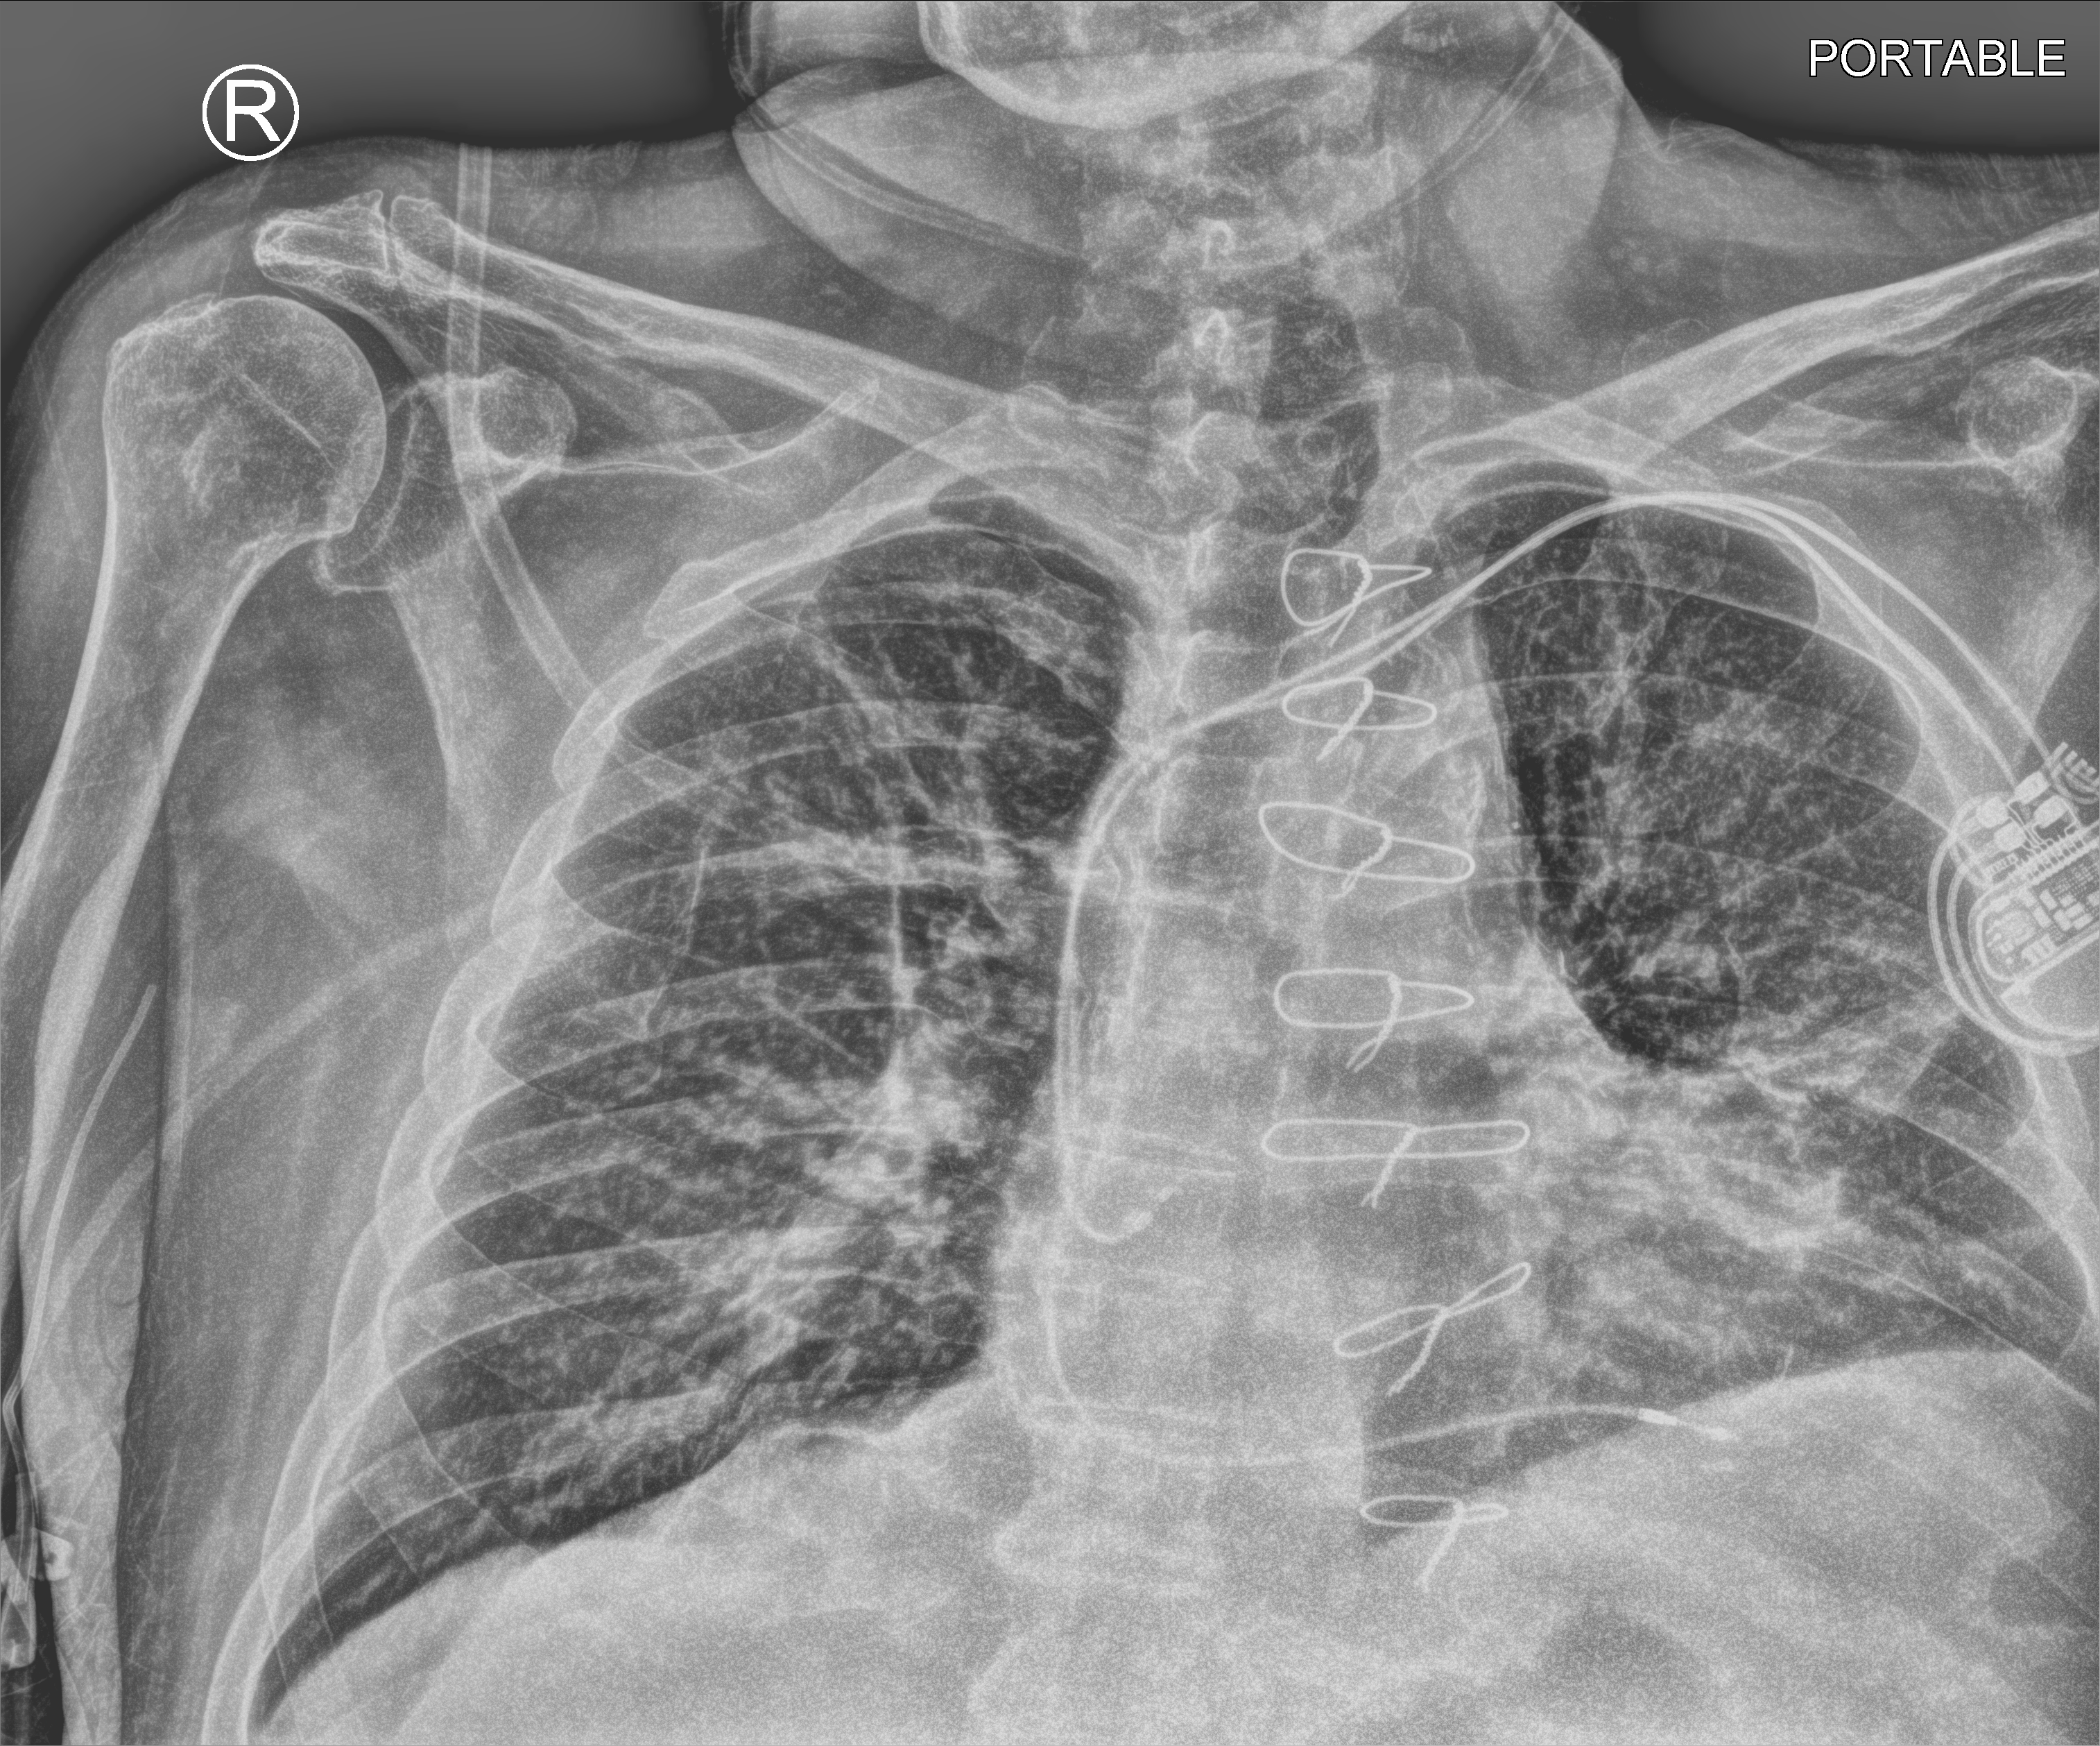
Chest X-ray (portable); anteroposterior (AP) projection. Patient hospitalised with COVID-19; male, aged 75–90 years.
From the hospital-stay record, not from the radiograph (when in the stay this image was taken is not recorded):
- mechanically ventilated during this hospital stay: no
- length of hospital stay: 6 days